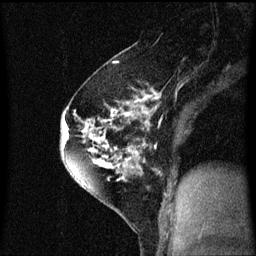
Breast MRI (dynamic contrast-enhanced), one sagittal slice. Position 37 of 60 along the scan axis. Dynamic contrast-enhanced series, image 2 of 3 at this slice position (ordered by acquisition). 1.5 T. TE 4.2 ms, TR 8.4 ms. 2 mm slice thickness. 256 × 256 image matrix. Female patient, age 60 years.
Structures marked on this image (semi-automatically segmented with operator editing):
- analysis volume of interest (the breast-tissue region the enhancement analysis was run in; not a lesion): bounding box <64,70,147,195> (left, top, right, bottom; pixels)
- tumour enhancement mask (voxels above the 70 % enhancement threshold inside the analysis volume of interest): <64,92,147,185>